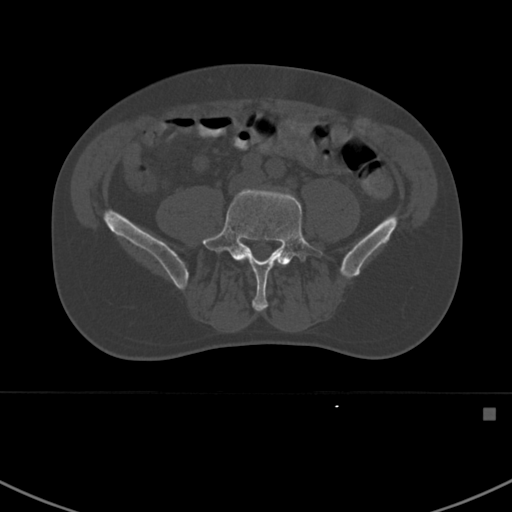
CT including the spine, one axial slice; position 223 of 412 along the scan axis; reconstruction kernel Br40s; bone window (W 1800 / L 400 HU); 1.5 mm slice thickness; 512 × 512 image matrix, field of view 358 × 358 mm. Male patient, age 59 years. Case-level facts recorded for this patient, not image findings: primary cancer: prostate.
Structures marked on this image (semi-automatically segmented with operator editing):
- L5 vertebra: bounding box [x1, y1, x2, y2] px = [202, 189, 324, 311]